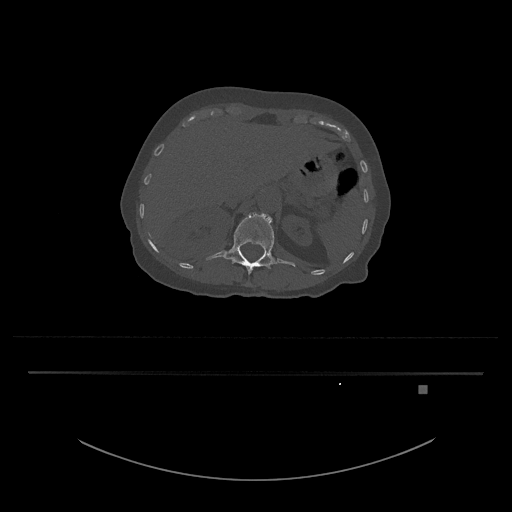
CT including the spine, one axial slice; position 554 of 797 along the scan axis; reconstruction kernel Br40s/3; 120 kVp; bone window (W 1800 / L 400 HU); 0.5 mm slice thickness; 512 × 512 image matrix, field of view 500 × 500 mm. Female patient, age 57 years. From the clinical record (not read from this slice): primary cancer: cervical.
Structures marked on this image (semi-automatically segmented with operator editing):
- L1 vertebra: bounding box [x1, y1, x2, y2] px = [206, 213, 295, 274]